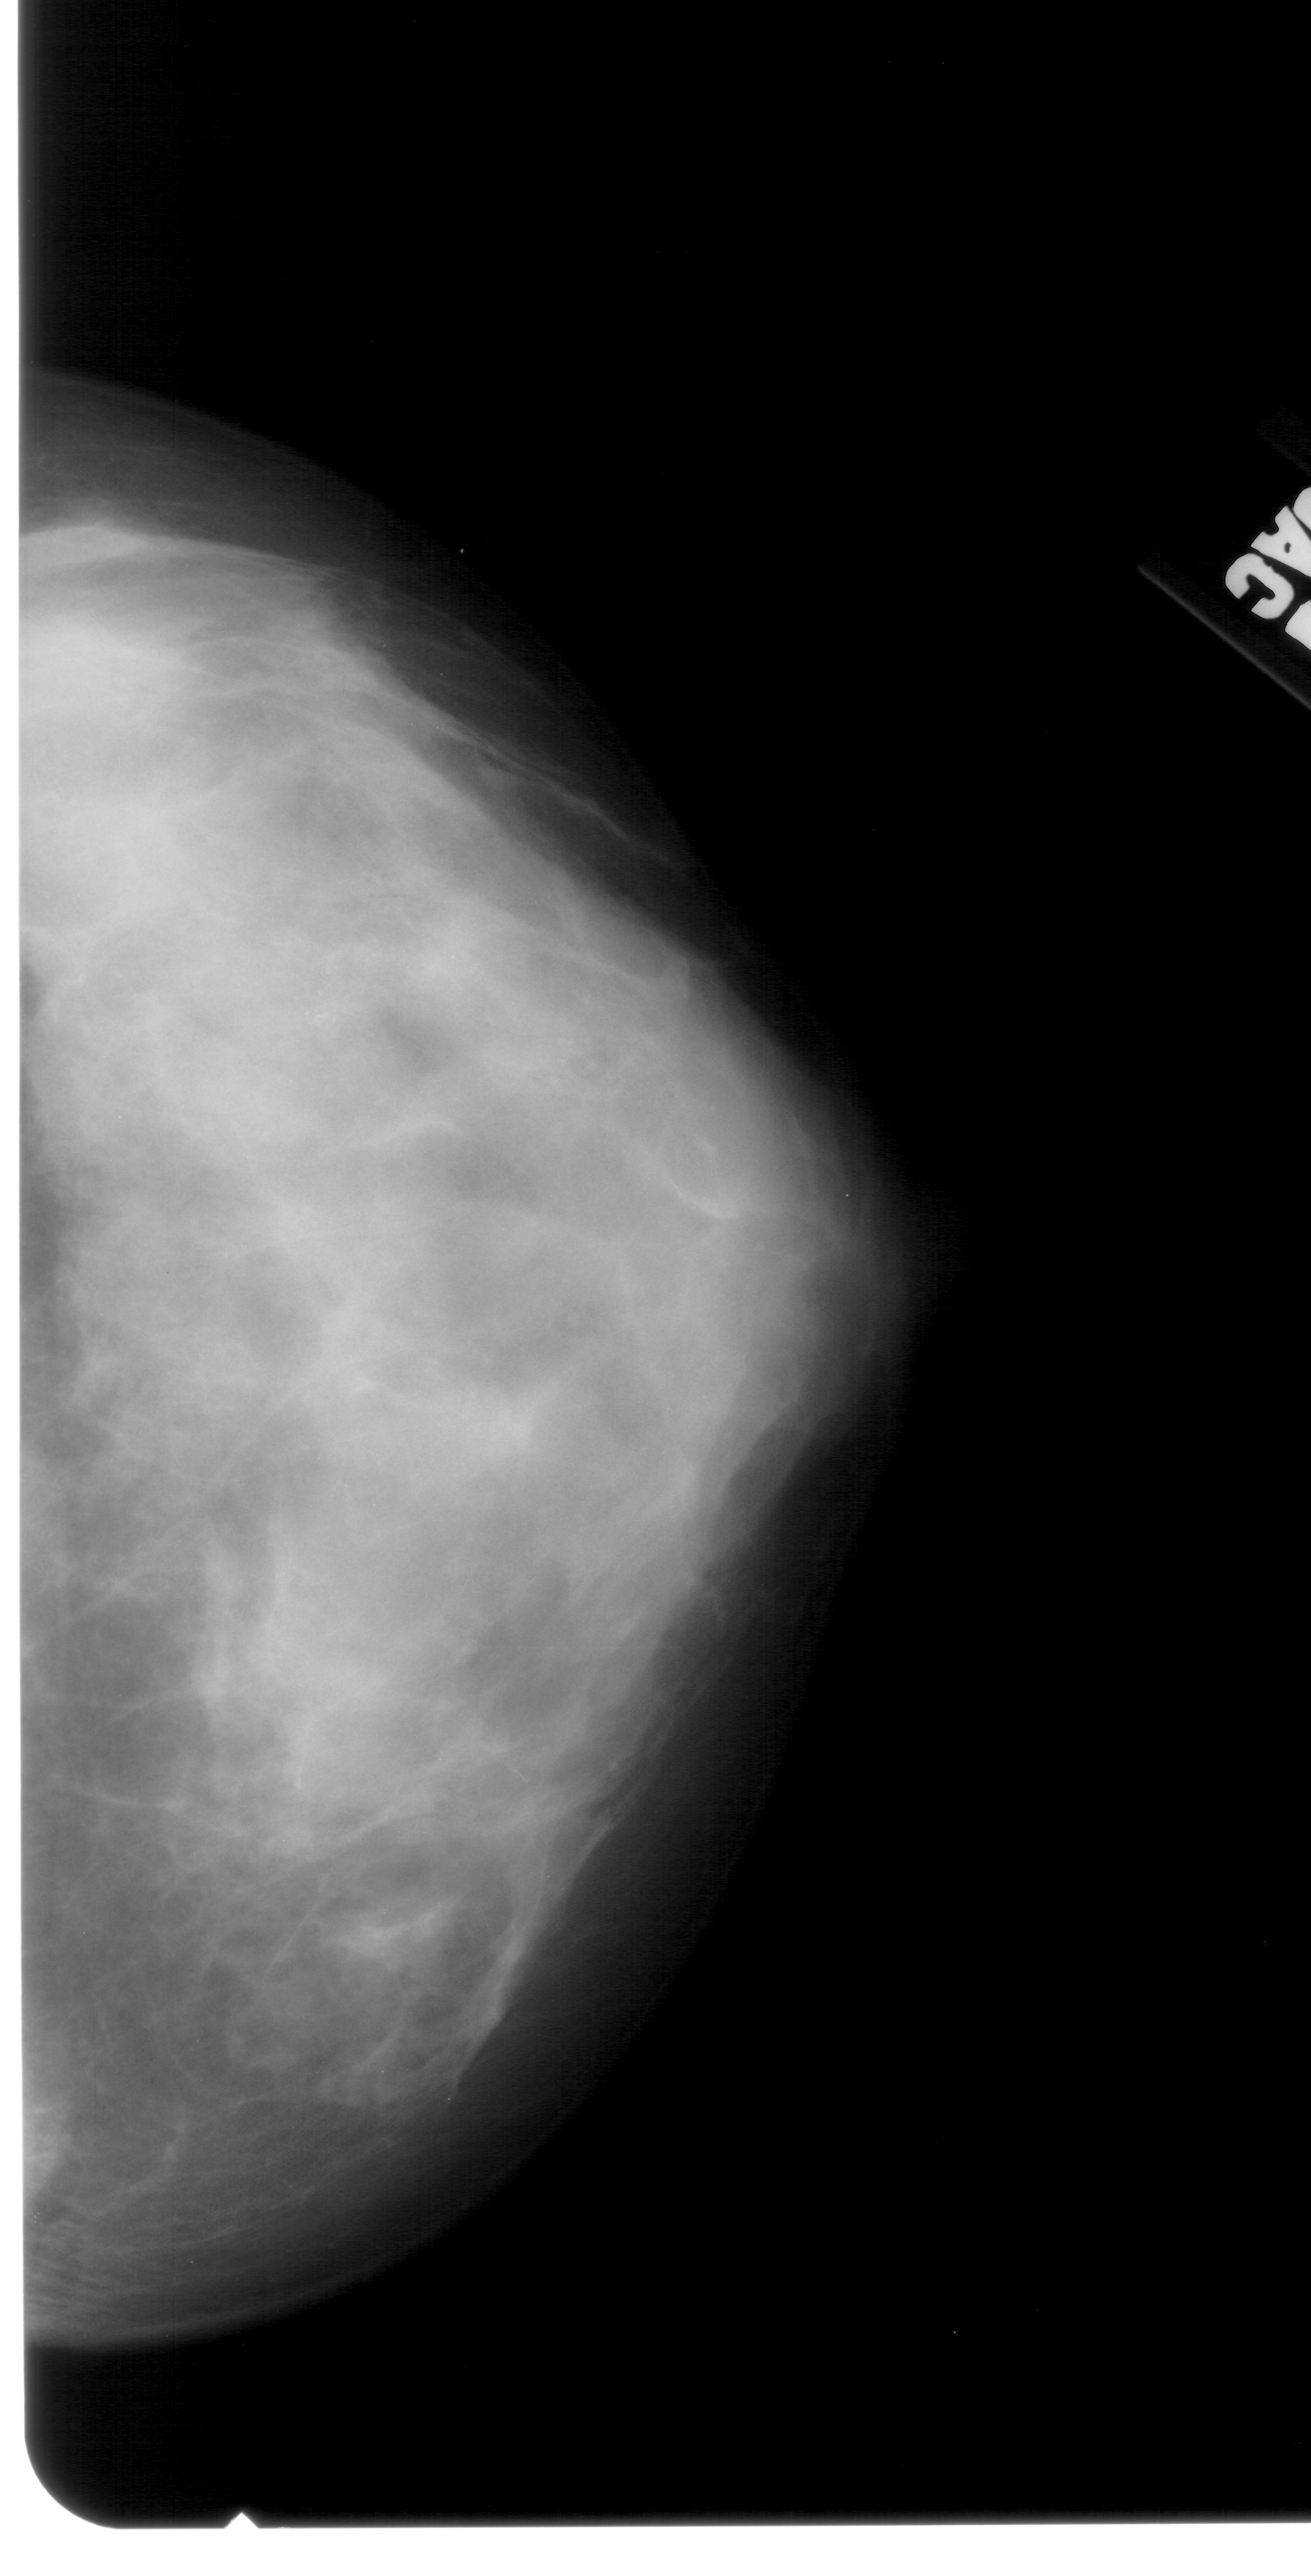
Mammogram (digitized film); right breast; CC view; 1311 × 2576 image matrix.
Expert-marked regions of interest on this image (one box per marked abnormality):
- calcifications, morphology pleomorphic, distribution clustered; BI-RADS assessment category 4; subtlety rating 4 on a 1 (subtle) to 5 (obvious) scale; pathology (as recorded): benign: box from (x=243, y=912) to (x=404, y=1089) px